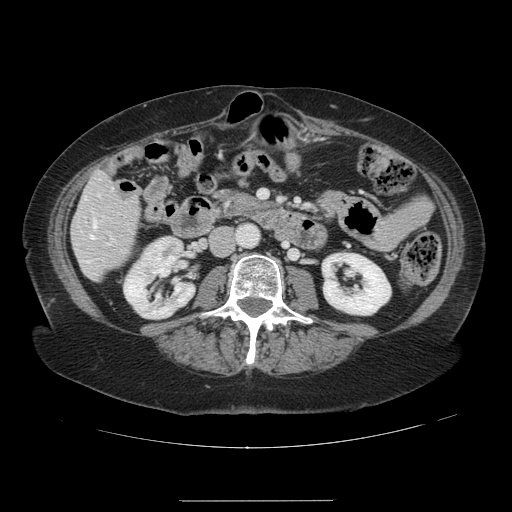
Contrast-enhanced abdominal CT, one axial slice. Slice 34 of 141 in the series (ordered by position). 120 kVp. Intravenous contrast given. Soft-tissue window (W 400 / L 40 HU). 2.5 mm slice thickness. 512 × 512 image matrix. Female patient, age 74 years. From the clinical record (not read from this slice): diagnosis: colorectal cancer liver metastases, imaged before liver resection; multiple liver metastases: yes; largest metastasis: 7 cm; chemotherapy before resection: no.
Annotated regions visible in this slice (outlined manually by an expert reader):
- hepatic veins: bounding box [x1, y1, x2, y2] px = [91, 218, 96, 238]
- liver: [72, 173, 140, 280]
- planned liver remnant (the part of the liver to remain after resection): [76, 173, 138, 280]